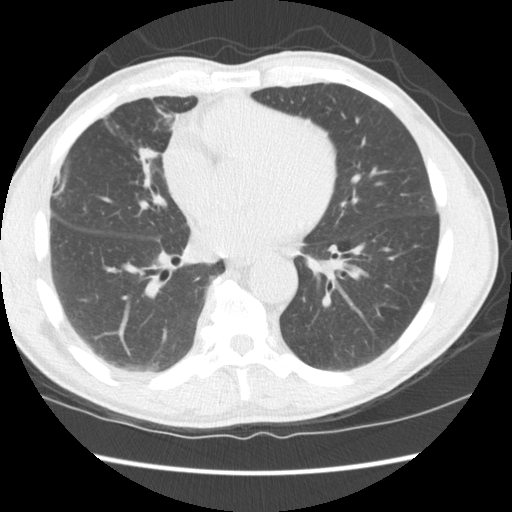
Low-dose screening chest CT, one axial slice; 120 kVp; lung window (W 1500 / L -600 HU); 512 × 512 image matrix, field of view 345 × 345 mm.
Structures marked on this image (manually delineated by an expert):
- lesion 1 (tumor, middle lobe of right lung): bounding box (x1, y1, x2, y2) in pixels: (143, 149, 157, 159)